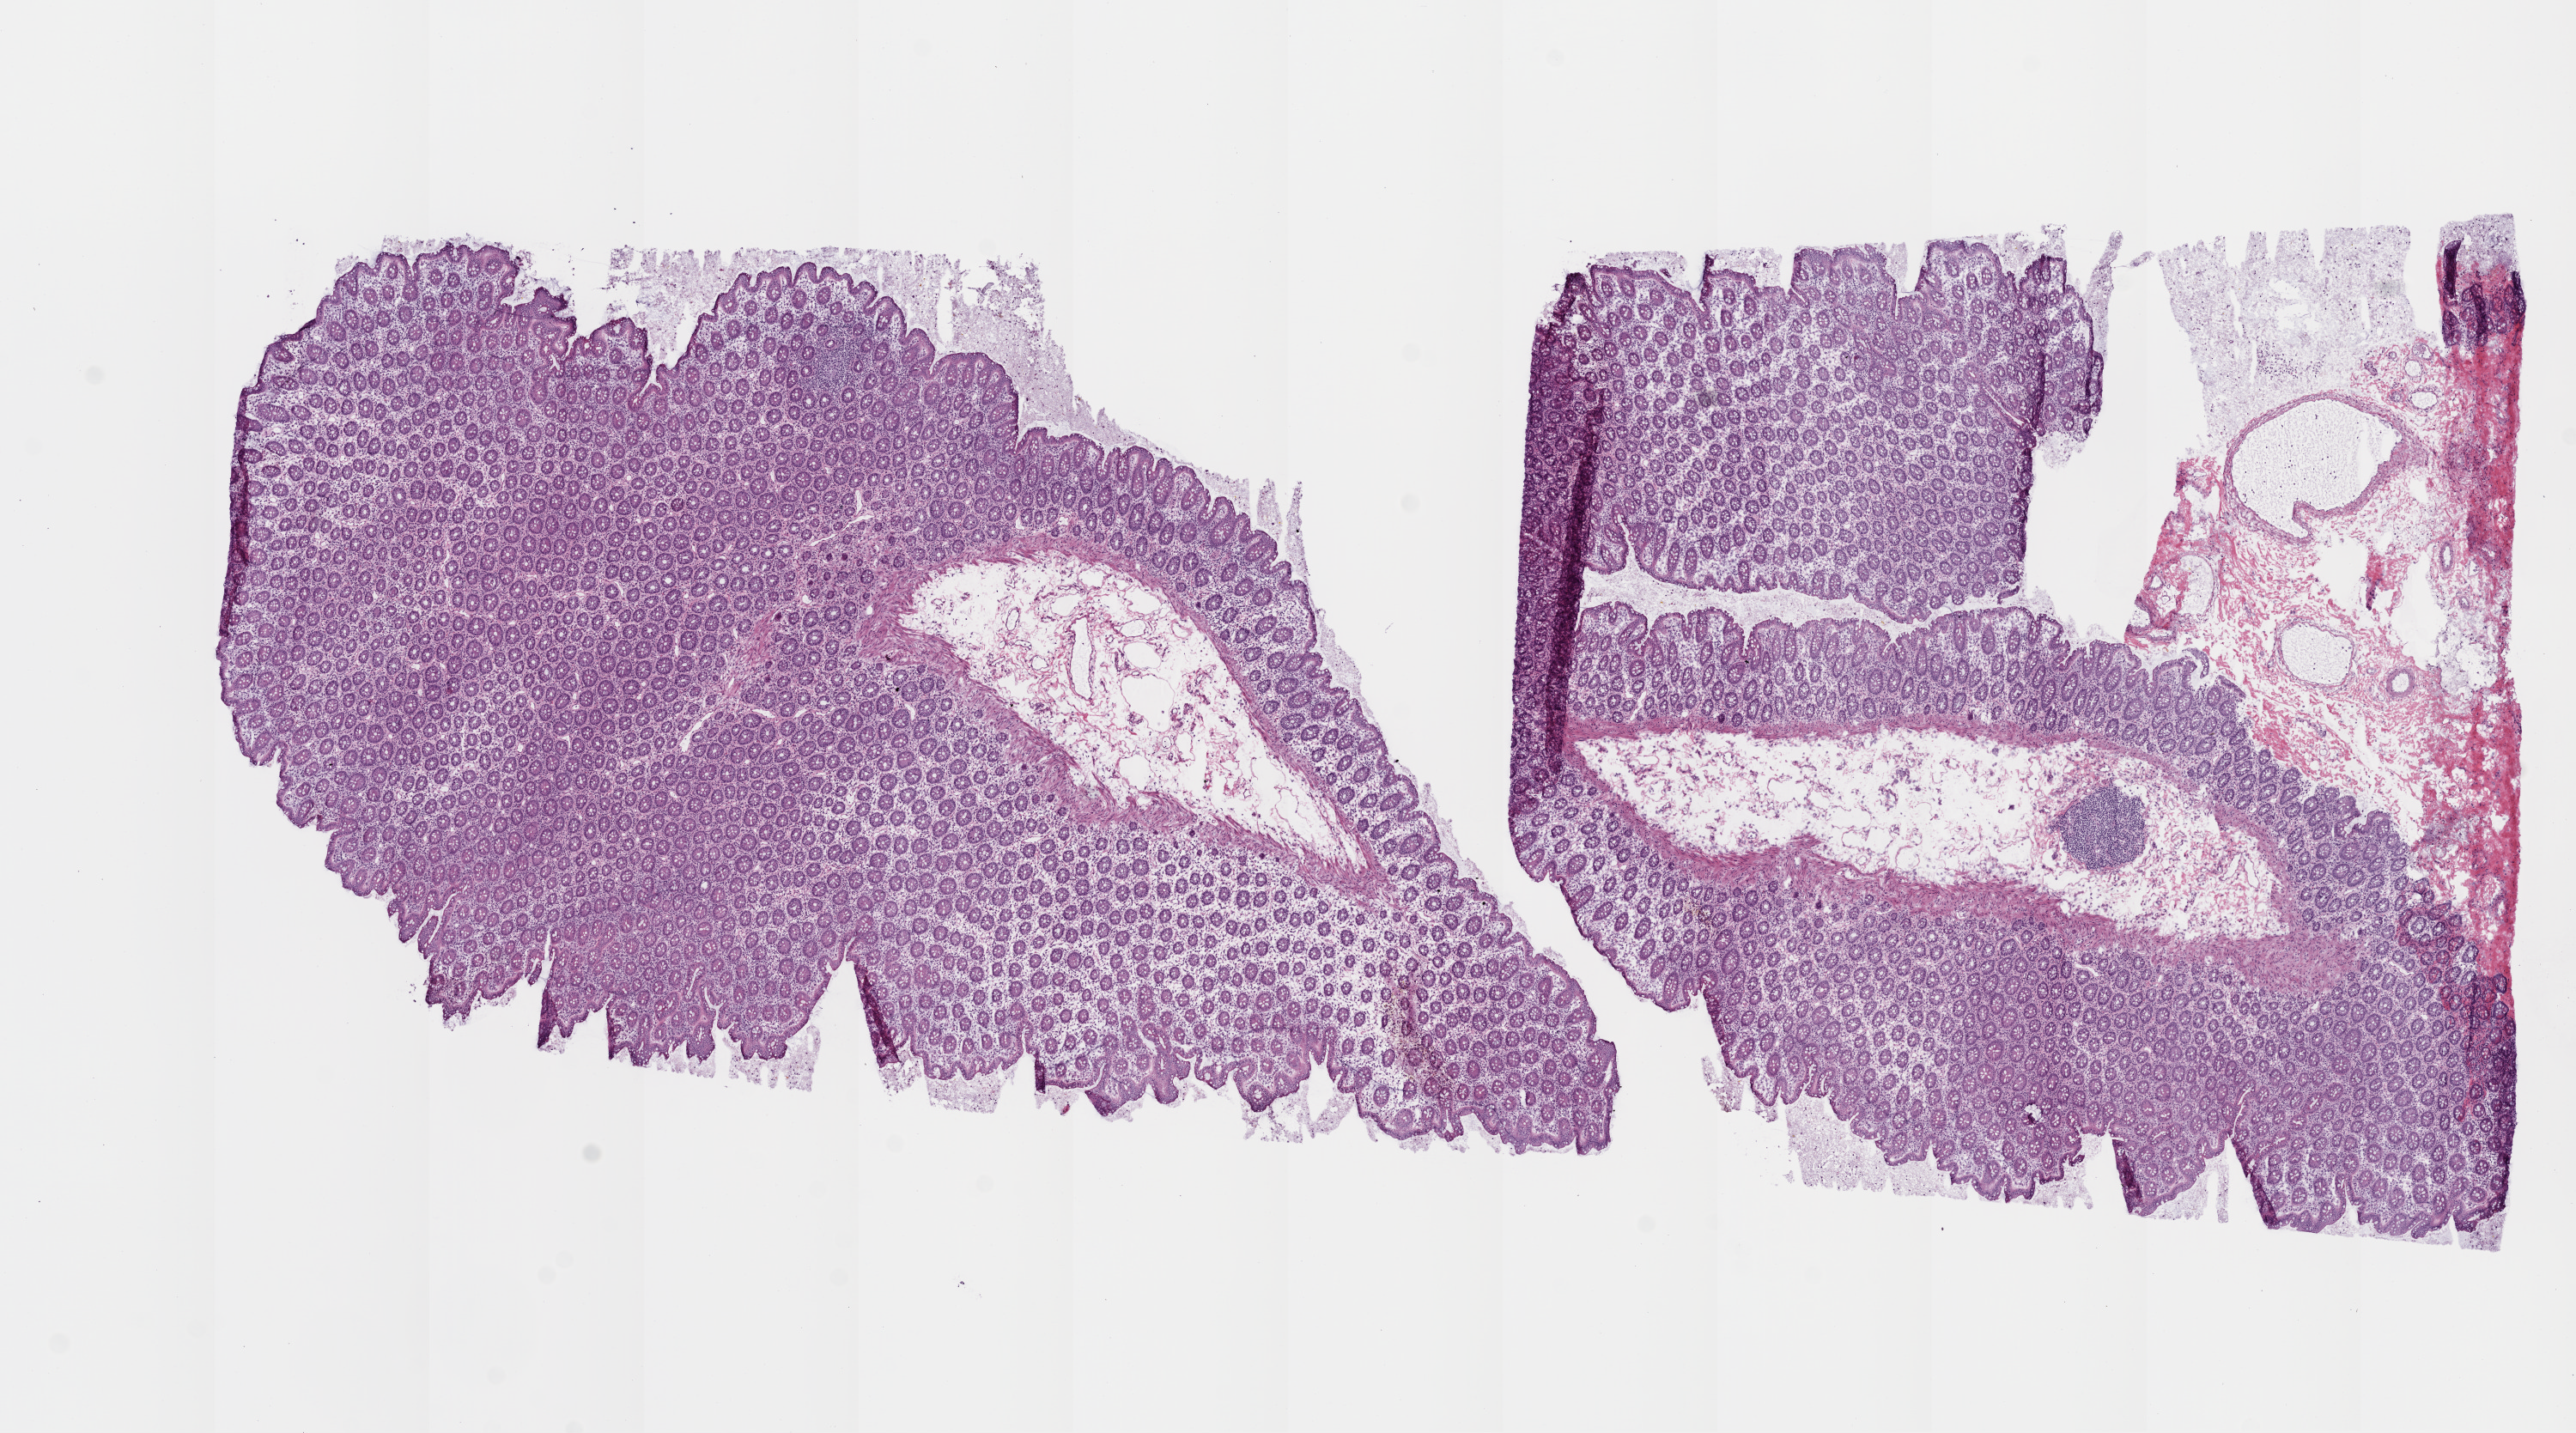
H&E whole-slide image, a low-resolution overview of the entire scanned area, about 12.0 x 6.7 mm. Frozen section from the top of the tissue portion. Colon, solid tissue normal (non-tumour tissue) sample. Female, age 57 years at initial diagnosis.
This section: solid tissue normal sample (biorepository sample class). Patient diagnosis: Adenocarcinoma, NOS (ascending colon).